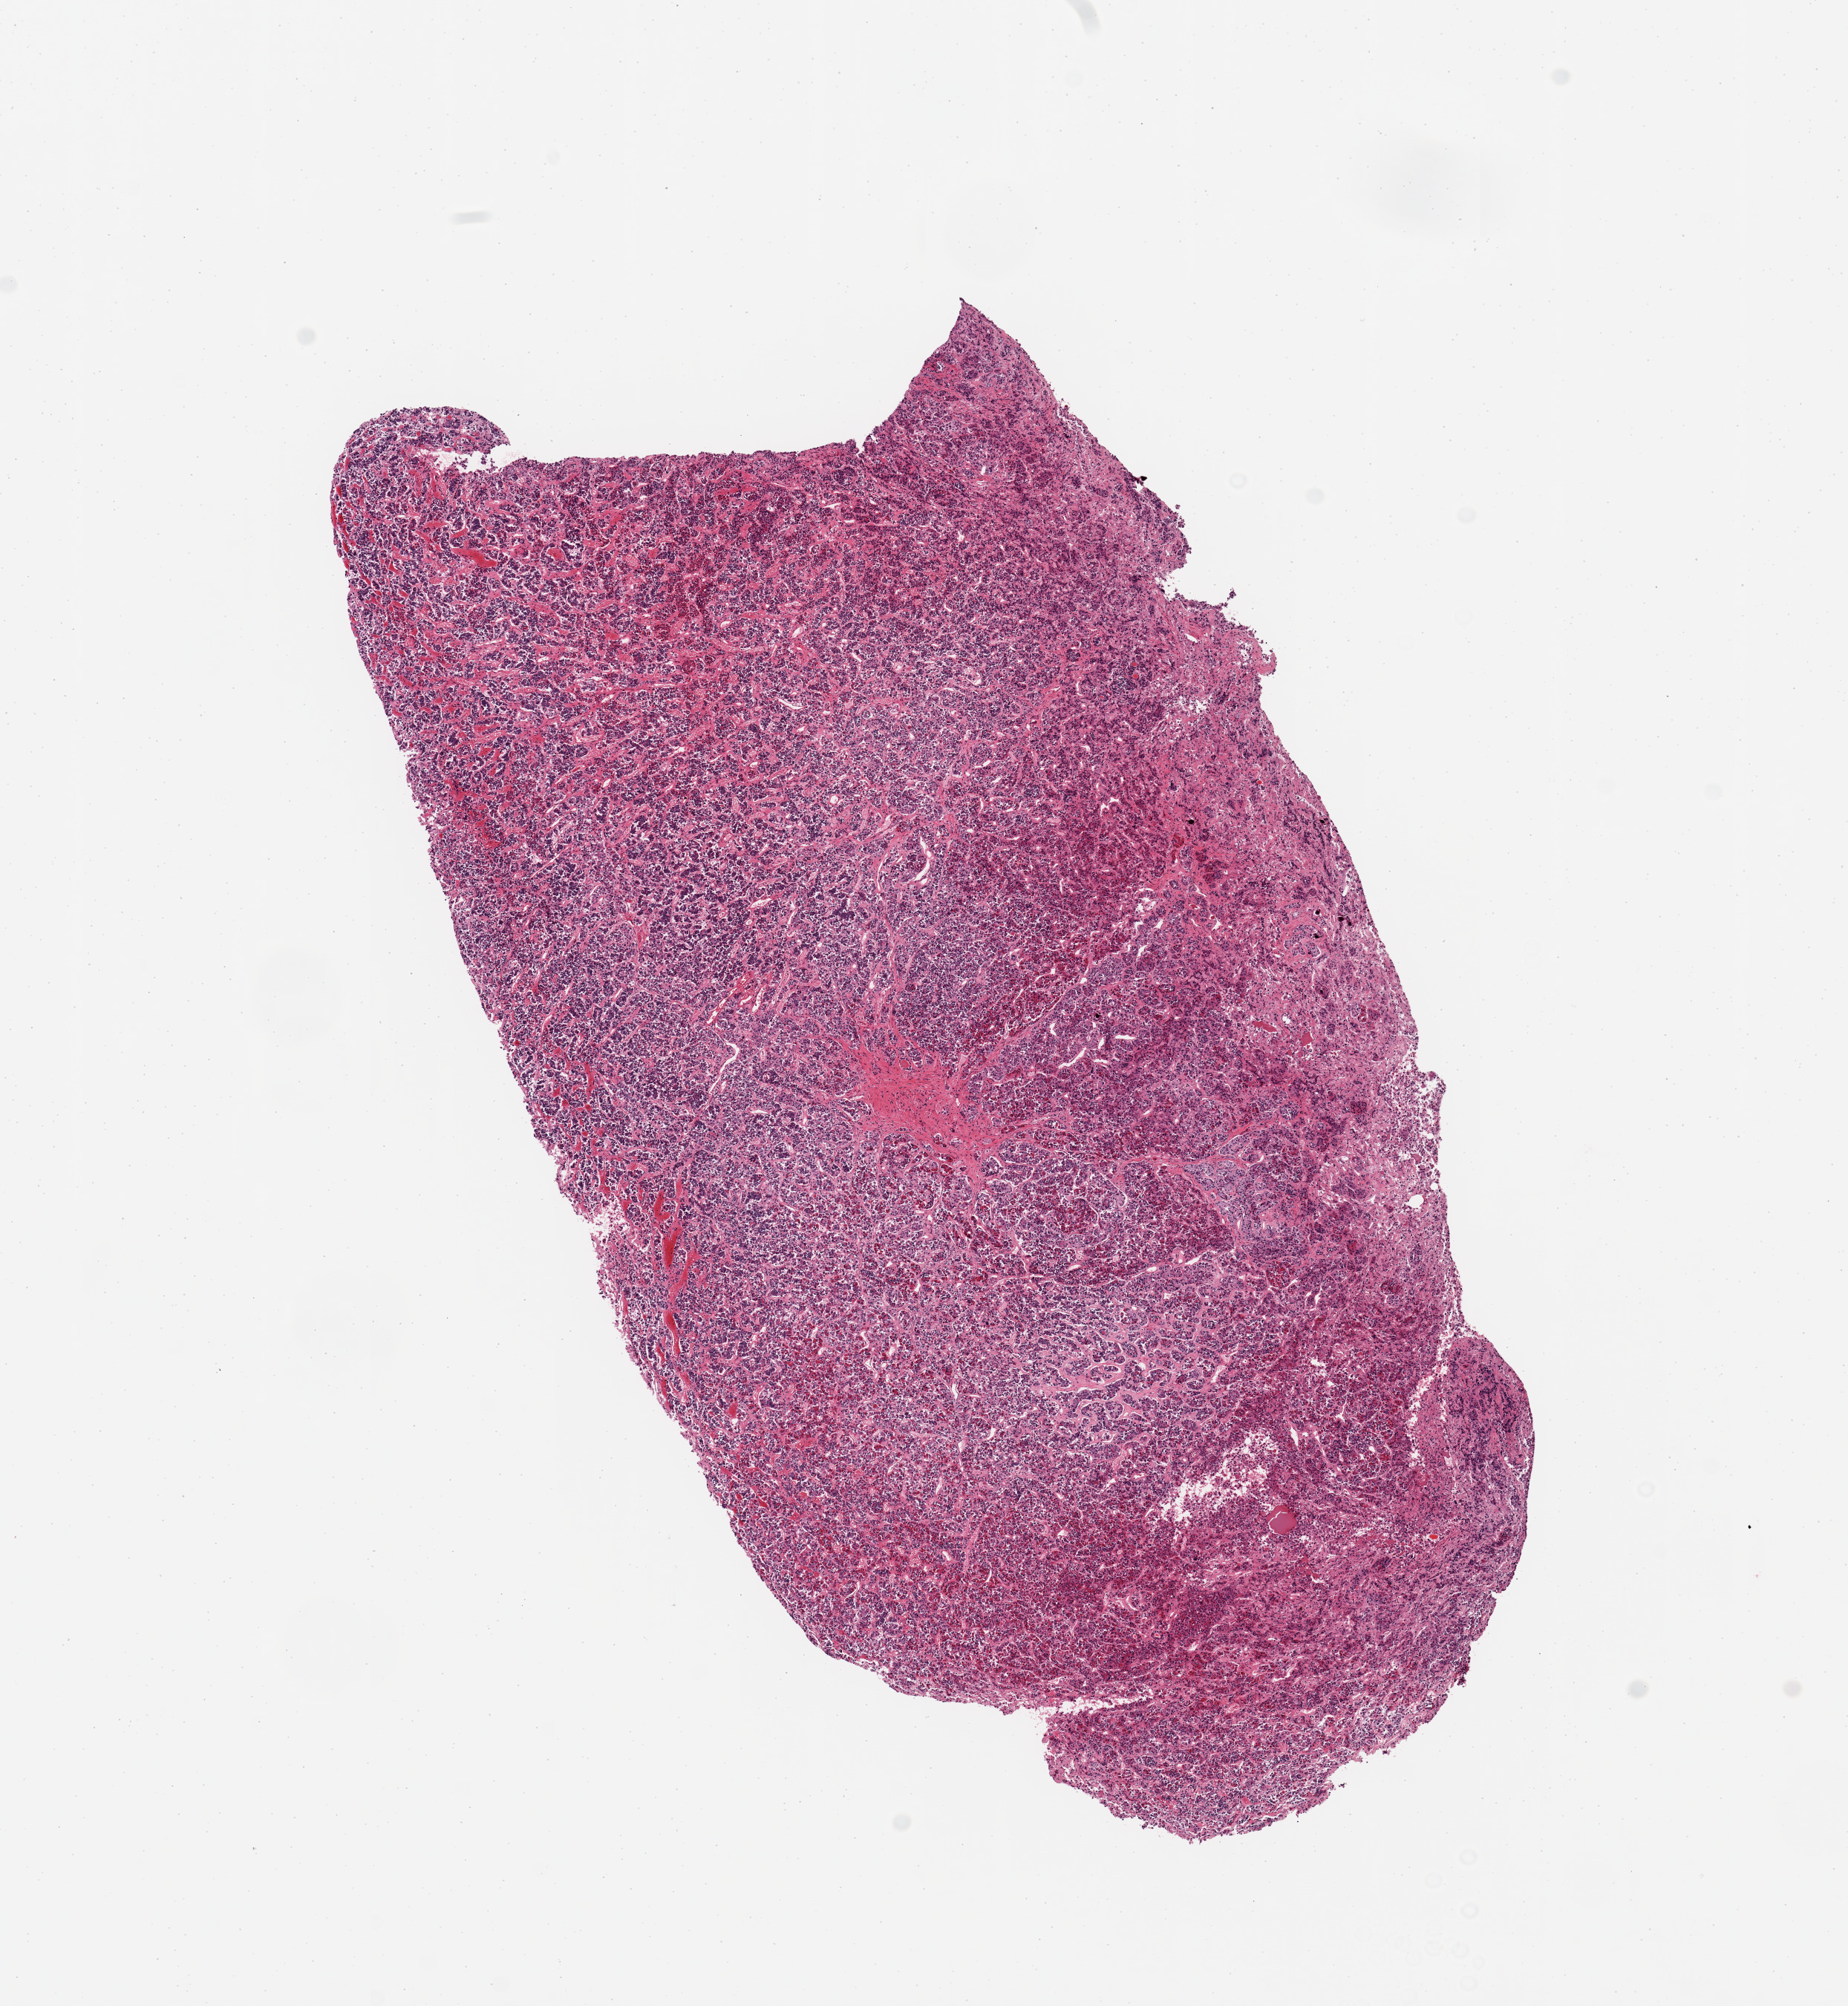
Whole-slide image, H&E stain — whole scanned area (about 9.8 x 10.7 mm) shown as a low-resolution overview, PAXgene-fixed paraffin-embedded (PFPE) section, sampled site (target tissue): pituitary, donor tissue sample. Donor: male.
Reviewer comment on this tissue sample: 1 piece, all adenohypophysis.